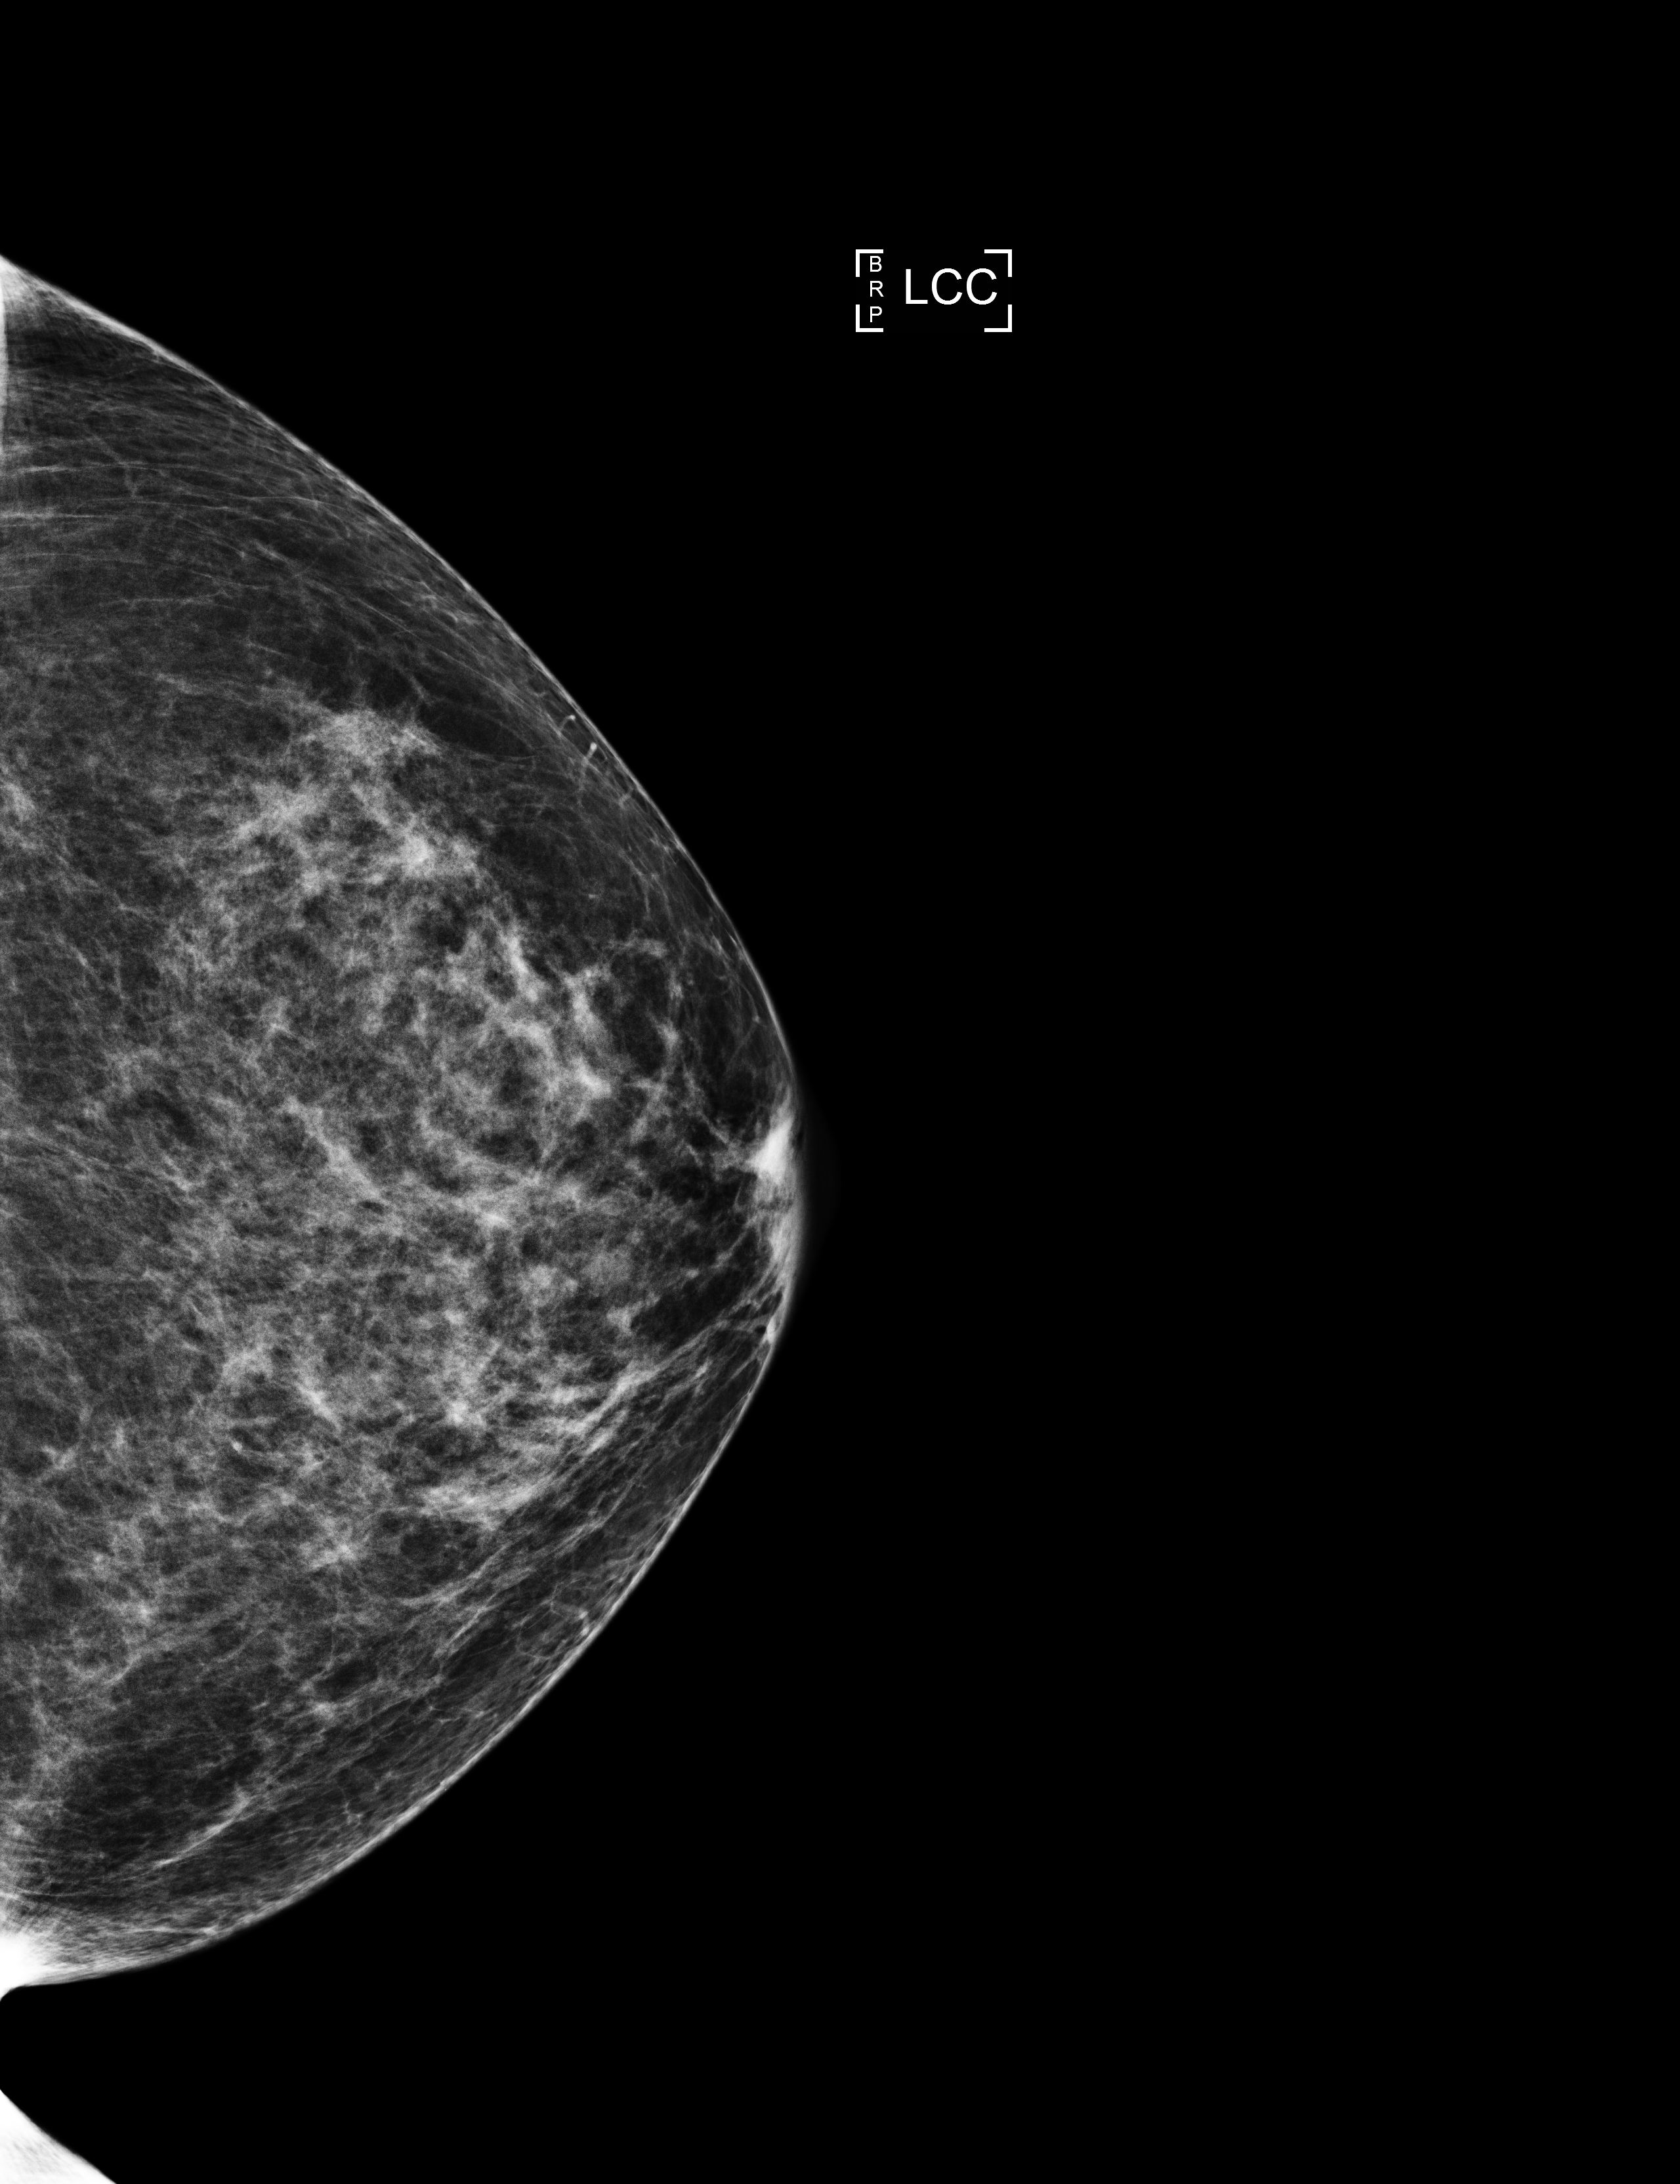
Full-field digital mammogram (FFDM), left breast, cranio-caudal projection, annual screening mammography examination, compressed breast thickness 64 mm, system: Selenia Dimensions. Patient aged 63 years (female).
Final BI-RADS assessment for this screening round (tomosynthesis exam, both breasts): category 2.